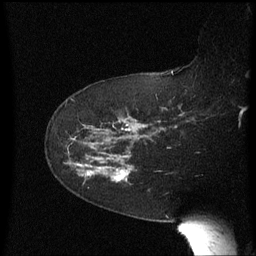
Breast MRI (dynamic contrast-enhanced), one sagittal slice; slice 42 of 60 in the series (ordered by position); dynamic contrast-enhanced series, image 2 of 3 at this slice position (ordered by acquisition); 1.5 T; TE 4.2 ms, TR 8.4 ms; 2.3 mm slice thickness; 256 × 256 image matrix. Female patient, age 63 years. From the clinical record (not read from this slice): setting: breast cancer imaged before/during neoadjuvant chemotherapy; receptor status: HER2-positive.
Structures marked on this image (semi-automatic segmentation, software-assisted and operator-edited):
- analysis volume of interest (the breast-tissue region the enhancement analysis was run in; not a lesion): box from (x=66, y=136) to (x=138, y=185) px
- tumour enhancement mask (voxels above the 70 % enhancement threshold inside the analysis volume of interest): (x=113, y=170)–(x=126, y=181)